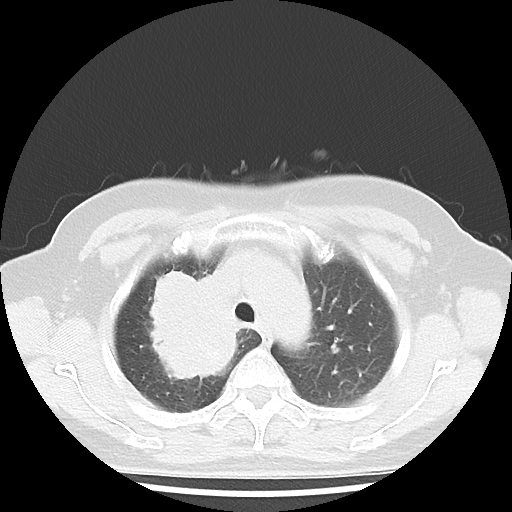
Chest CT, one axial slice; position 33 of 43 along the scan axis; lung window (W 1500 / L -600 HU); 5 mm slice thickness; 512 × 512 image matrix, field of view 316 × 316 mm. Female patient, age 62 years. From the clinical record (not read from this slice): clinical TNM (as recorded): T3 N0 M0; histopathological grade: G3.
Annotated regions visible in this slice (rectangle marked by the reading radiologist):
- lung tumour (recorded histology: small cell carcinoma): bounding box (x1, y1, x2, y2) in pixels: (138, 253, 242, 394)